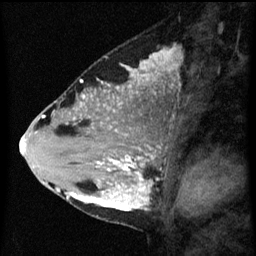
Breast MRI (dynamic contrast-enhanced), one sagittal slice; position 26 of 60 along the scan axis; dynamic contrast-enhanced series, image 2 of 3 at this slice position (ordered by acquisition); 1.5 T; TE 4.2 ms, TR 8 ms; 2.3 mm slice thickness; 256 × 256 image matrix, field of view 180 × 180 mm. Patient: female, 33 years.
Structures marked on this image (semi-automatically segmented with operator editing):
- analysis volume of interest (the breast-tissue region the enhancement analysis was run in; not a lesion): box from (x=71, y=118) to (x=166, y=217) px
- tumour enhancement mask (voxels above the 70 % enhancement threshold inside the analysis volume of interest): (x=71, y=130)–(x=160, y=211)